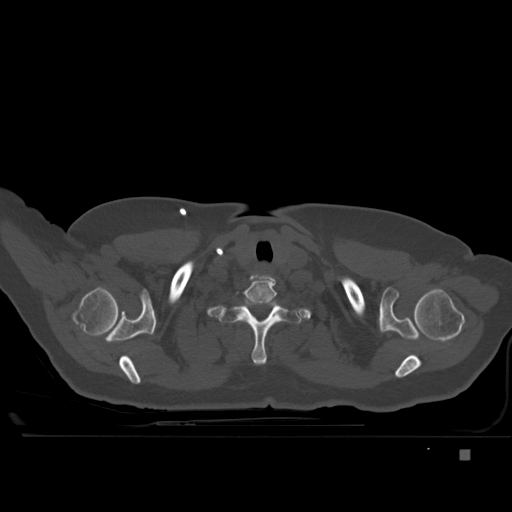
CT including the spine, one axial slice; position 405 of 477 along the scan axis; bone window (W 1800 / L 400 HU); 1.5 mm slice thickness; 512 × 512 image matrix, field of view 422 × 422 mm. Patient: female, 74 years. From the clinical record (not read from this slice): primary cancer: colon.
Outlined on this slice (semi-automatic segmentation, software-assisted and operator-edited):
- T1 vertebra: bounding box [x1, y1, x2, y2] px = [234, 297, 287, 365]